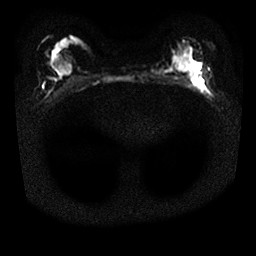
Breast MRI, one axial slice. Position 15 of 25 along the scan axis. Diffusion-weighted series; image 2 of 4 stored at this slice position (different b-values; order by instance number). 1.5 T. 4 mm slice thickness. 256 × 256 image matrix. Female patient.
Outlined on this slice (expert manual segmentation):
- tumour on diffusion-weighted imaging: bounding box [x1, y1, x2, y2] px = [192, 75, 204, 84]